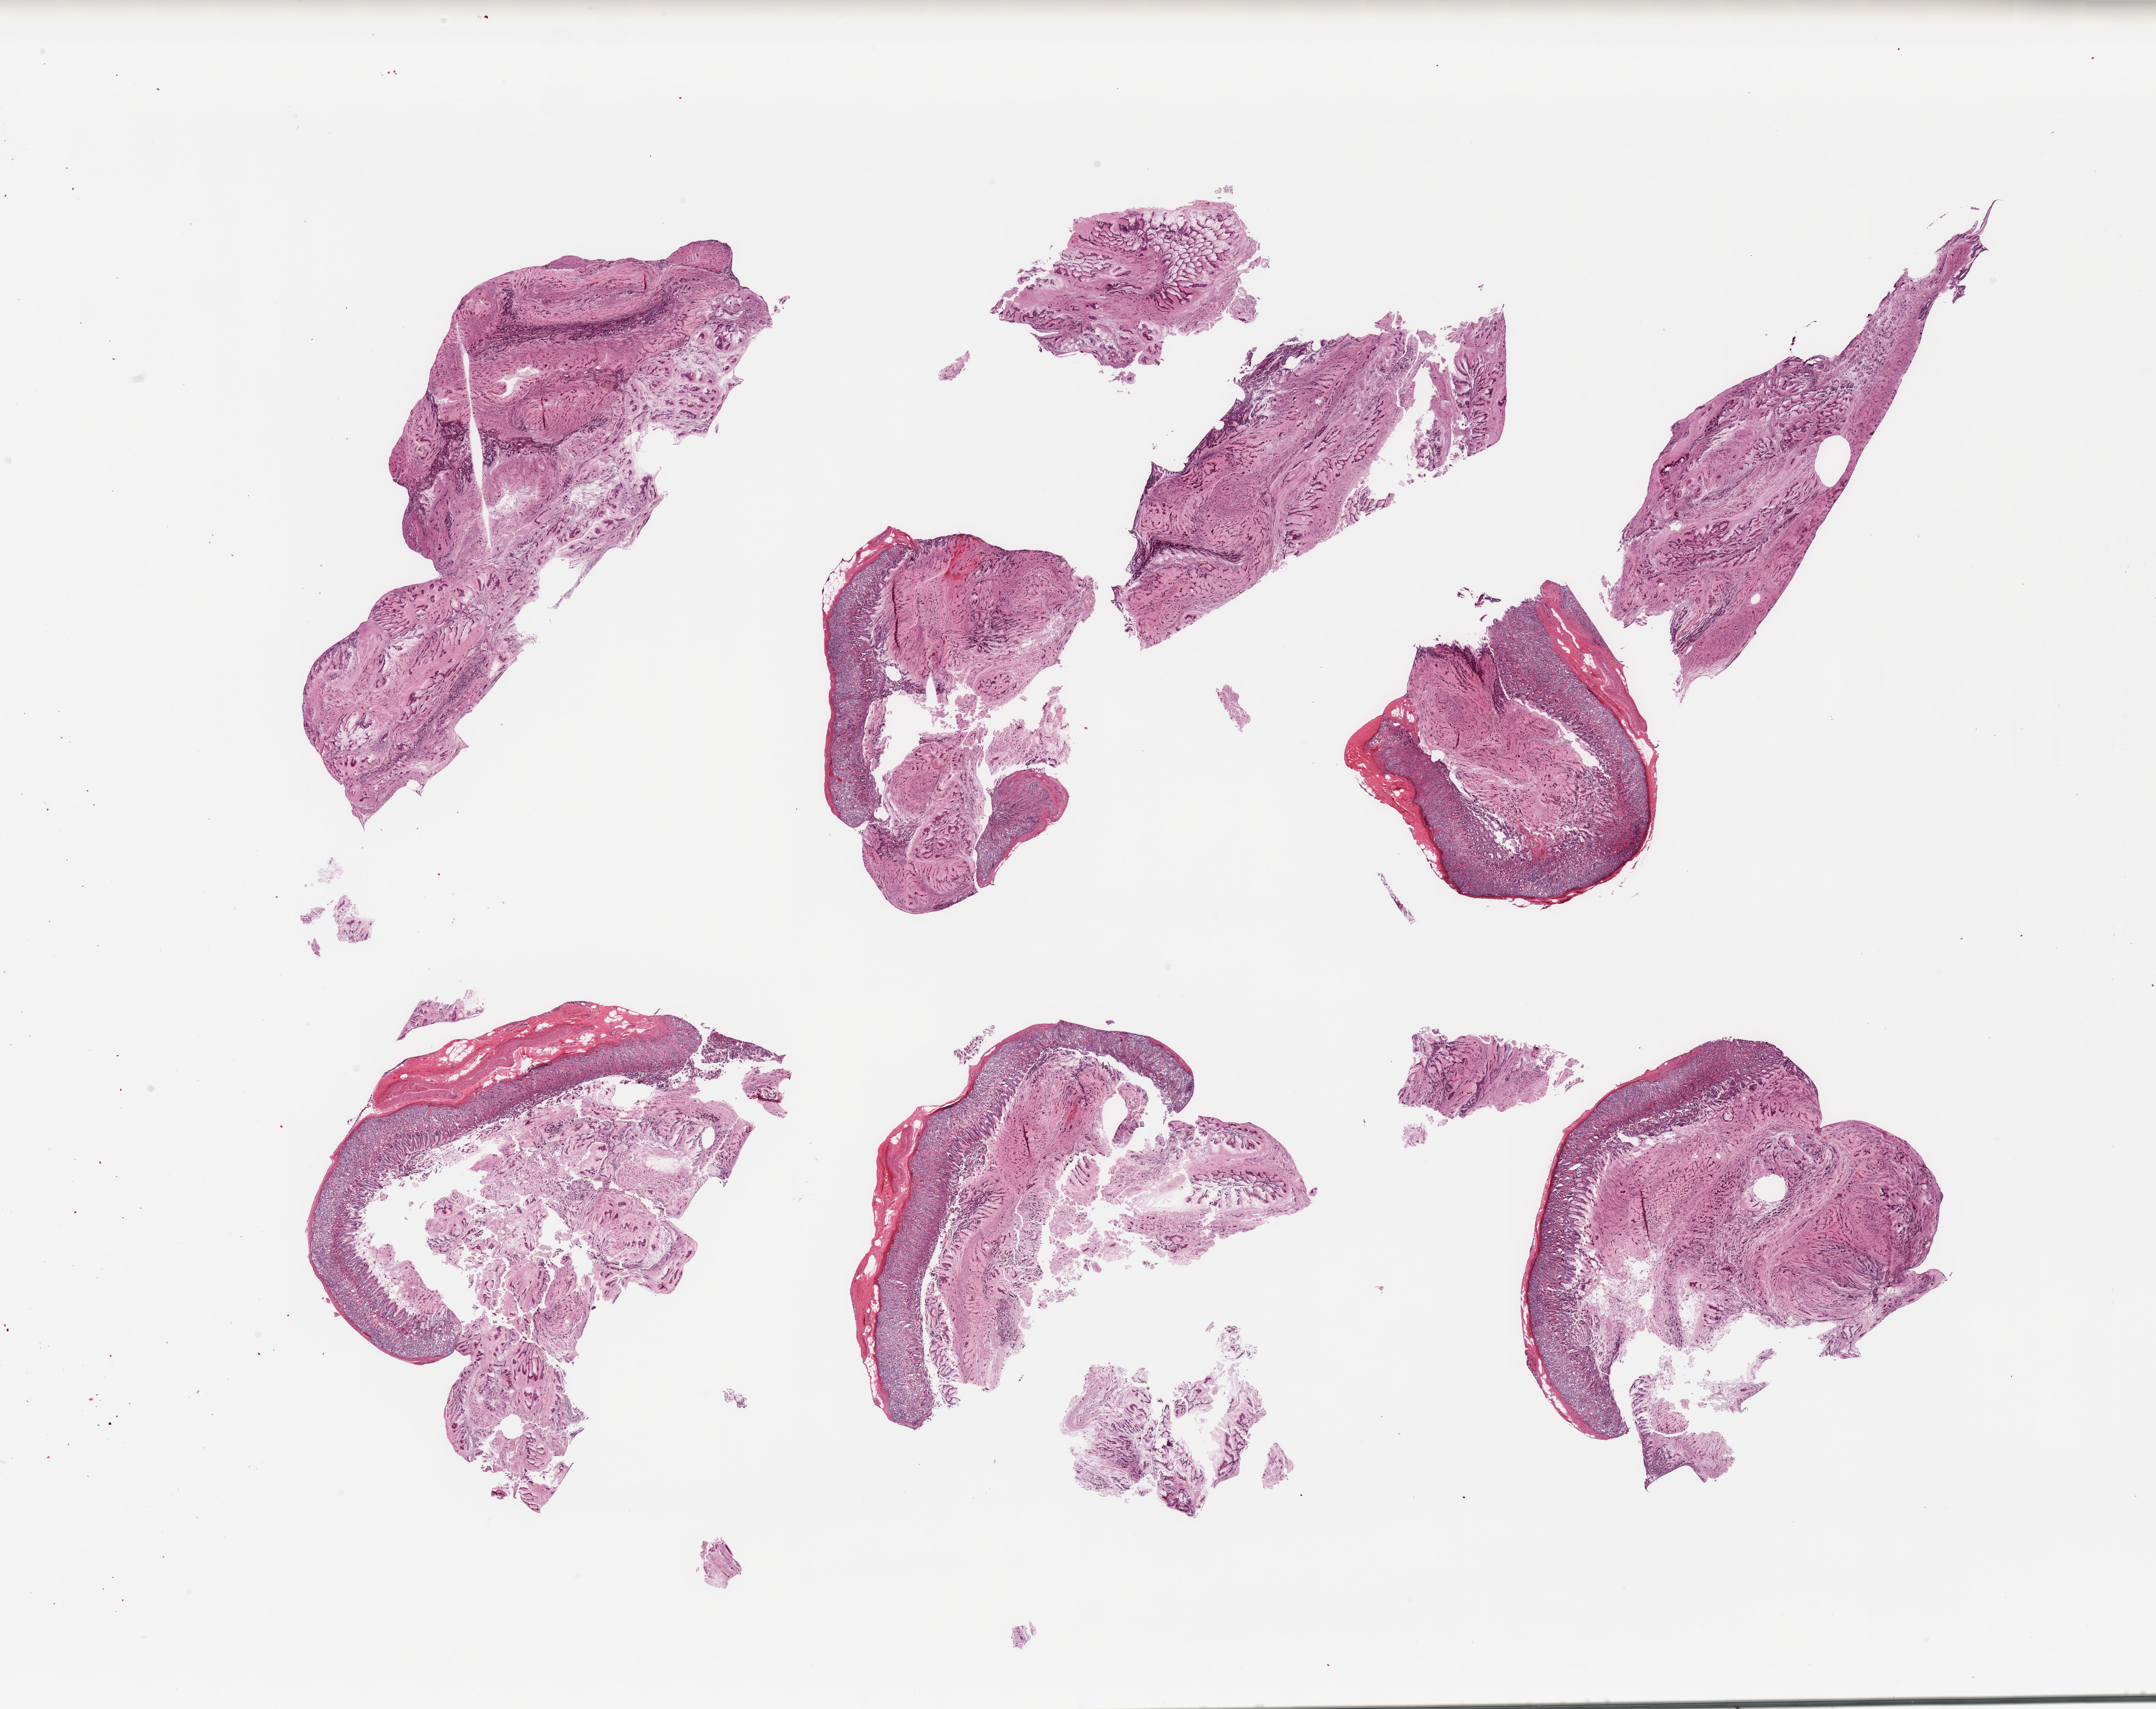
Digitized hematoxylin and eosin (H&E)-stained section, shown as a low-resolution overview of the whole scanned area (about 29.5 x 23.4 mm). PAXgene-fixed paraffin-embedded (PFPE) section. Section of stomach (target tissue). Donor tissue sample.
Pathologist's review note for this sample: 6 pieces (fragmented), target mucosa up to ~0.8mm, advanced autolysis/sloughing.